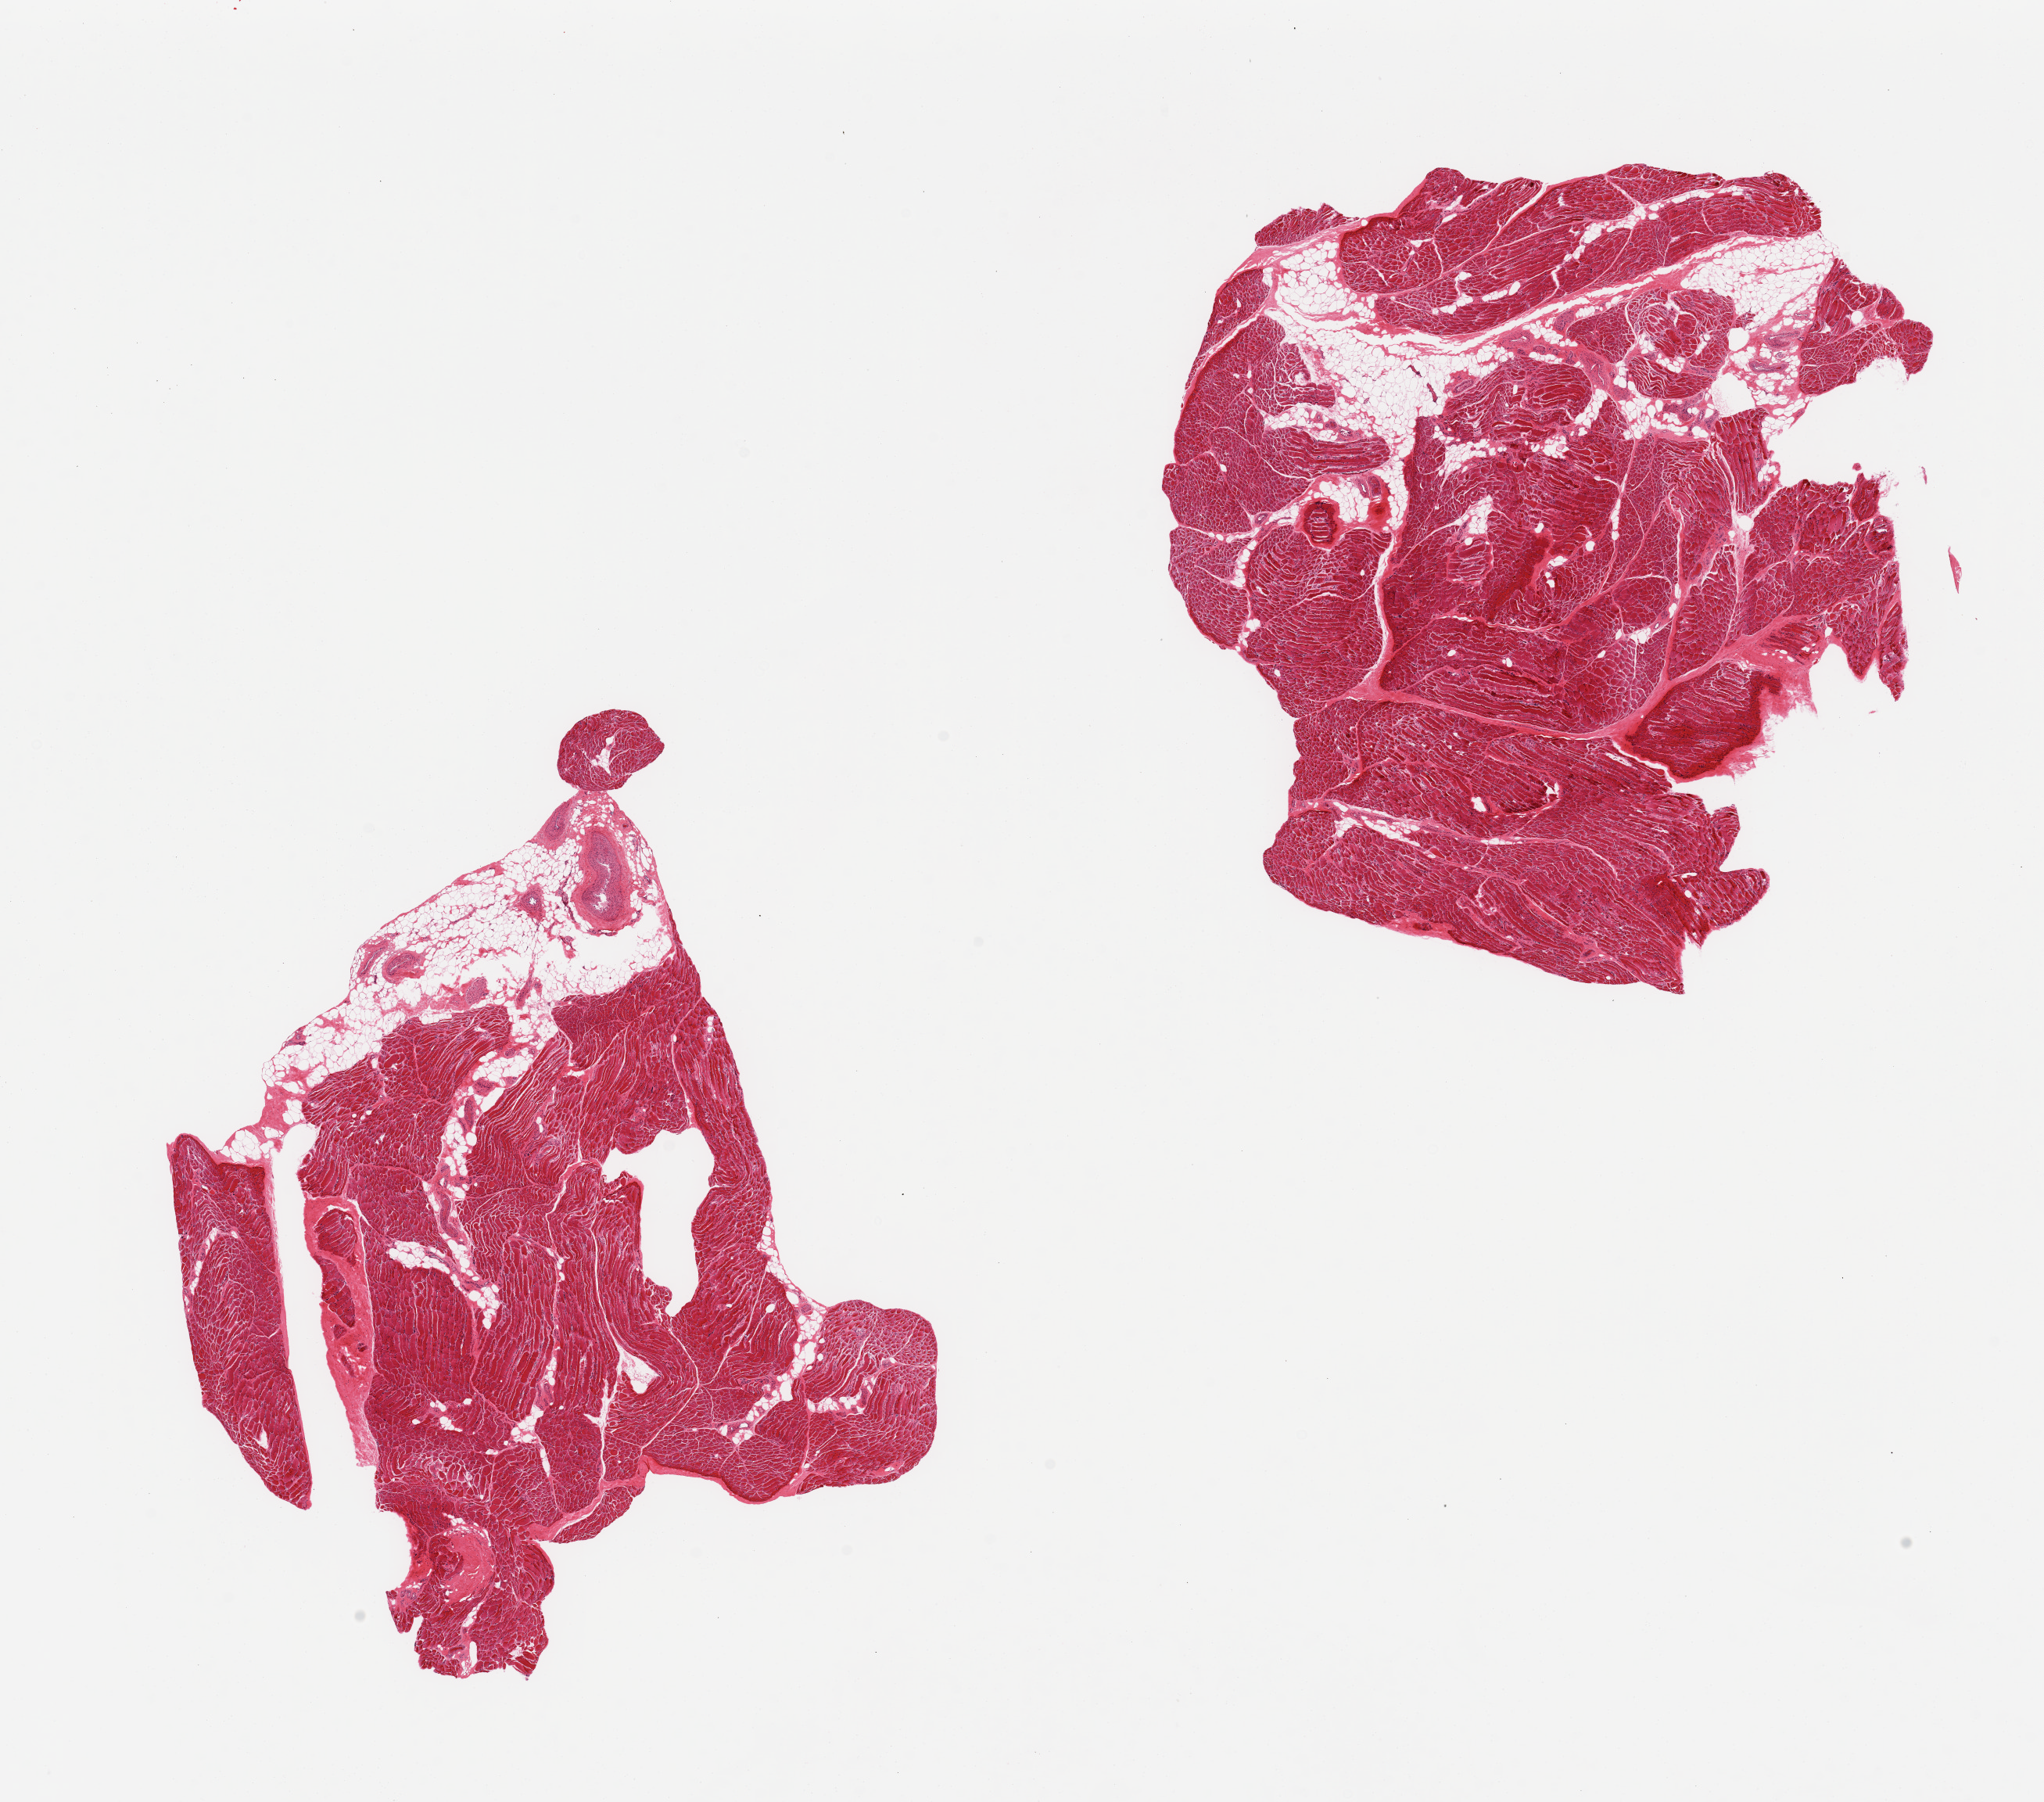
Digitized H&E-stained section, shown as a low-resolution overview of the whole scanned area (about 20.7 x 18.2 mm, slide scanned at 20x); PAXgene-fixed, paraffin-embedded tissue; target tissue: skeletal muscle; donor tissue sample. Male donor.
Reviewer comment on this tissue sample: 2 pieces, 10-20% interstitial fat/vascular elements.